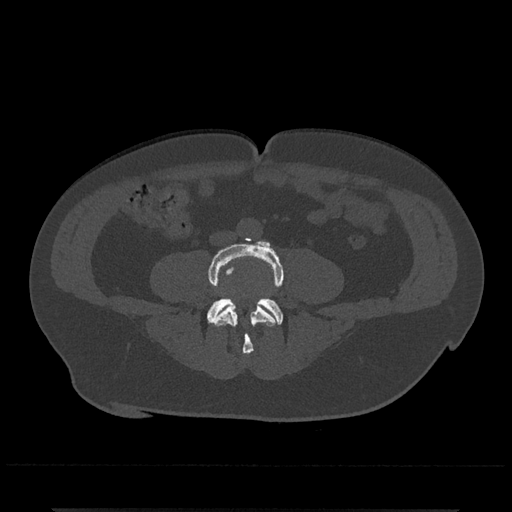
CT including the spine, one axial slice. Position 126 of 797 along the scan axis. Reconstruction kernel Br40s/3. Bone window (W 1800 / L 400 HU). 0.5 mm slice thickness. 512 × 512 image matrix. Patient: male, 67 years. From the clinical record (not read from this slice): primary cancer: prostate.
Annotated regions visible in this slice (semi-automatically segmented with operator editing):
- L4 vertebra: bounding box [x1, y1, x2, y2] px = [208, 240, 283, 355]
- L5 vertebra: [207, 297, 283, 324]